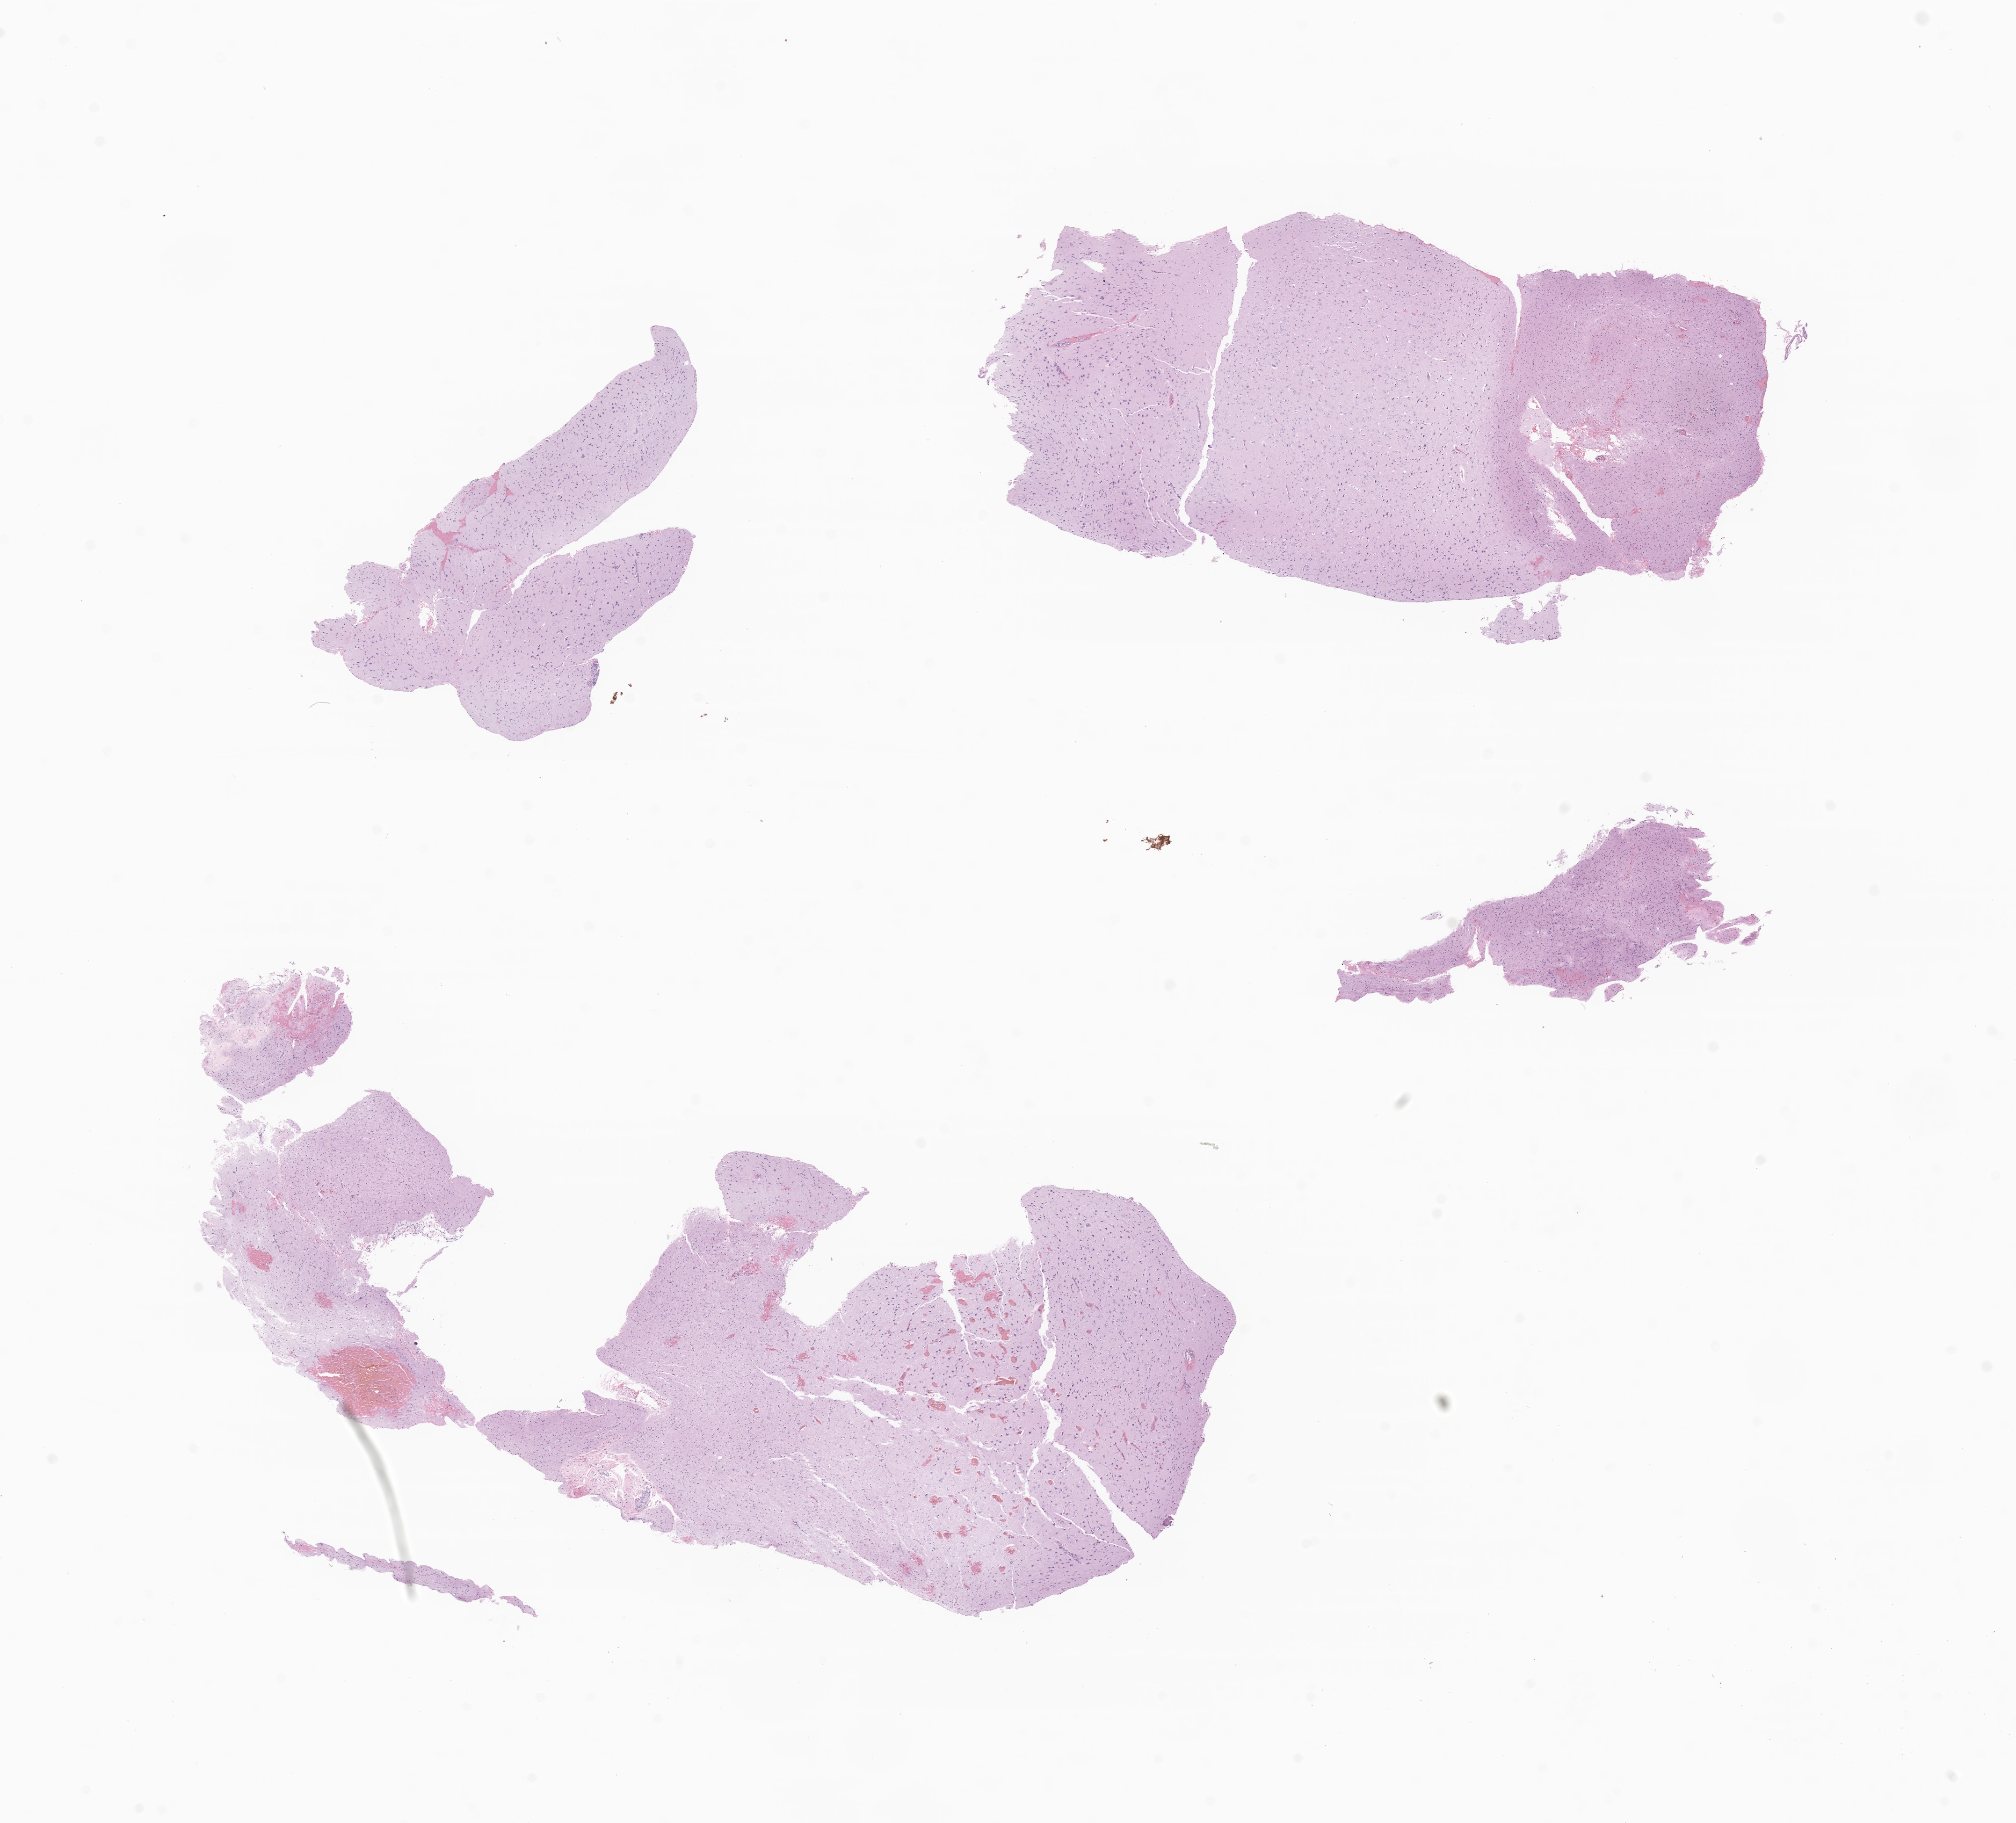
Whole-slide image, haematoxylin and eosin stain of tumor tissue from the brain, whole scanned area (about 18.2 x 16.4 mm) shown as a low-resolution overview. FFPE section. Male patient, age 126 months.
Diagnosis: Neoplasm, malignant.